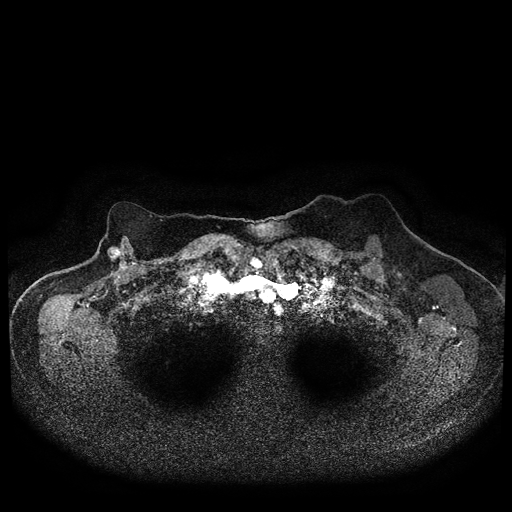
Breast MRI (dynamic contrast-enhanced, multi-phase), one axial slice. Position 81 of 116 along the scan axis. Dynamic contrast-enhanced series, time point 2 of 5 at this slice position (early post-contrast). 1.5 T. TE 2.7 ms, TR 5.4 ms. 512 × 512 image matrix, field of view 340 × 340 mm. Patient: female, 72 years.
Outlined on this slice (semi-automatically segmented with operator editing):
- breast lesion (labelled 'tumour' in the annotation; benign lesions carry a separate 'benign' label): bounding box [x1, y1, x2, y2] px = [107, 245, 121, 262]